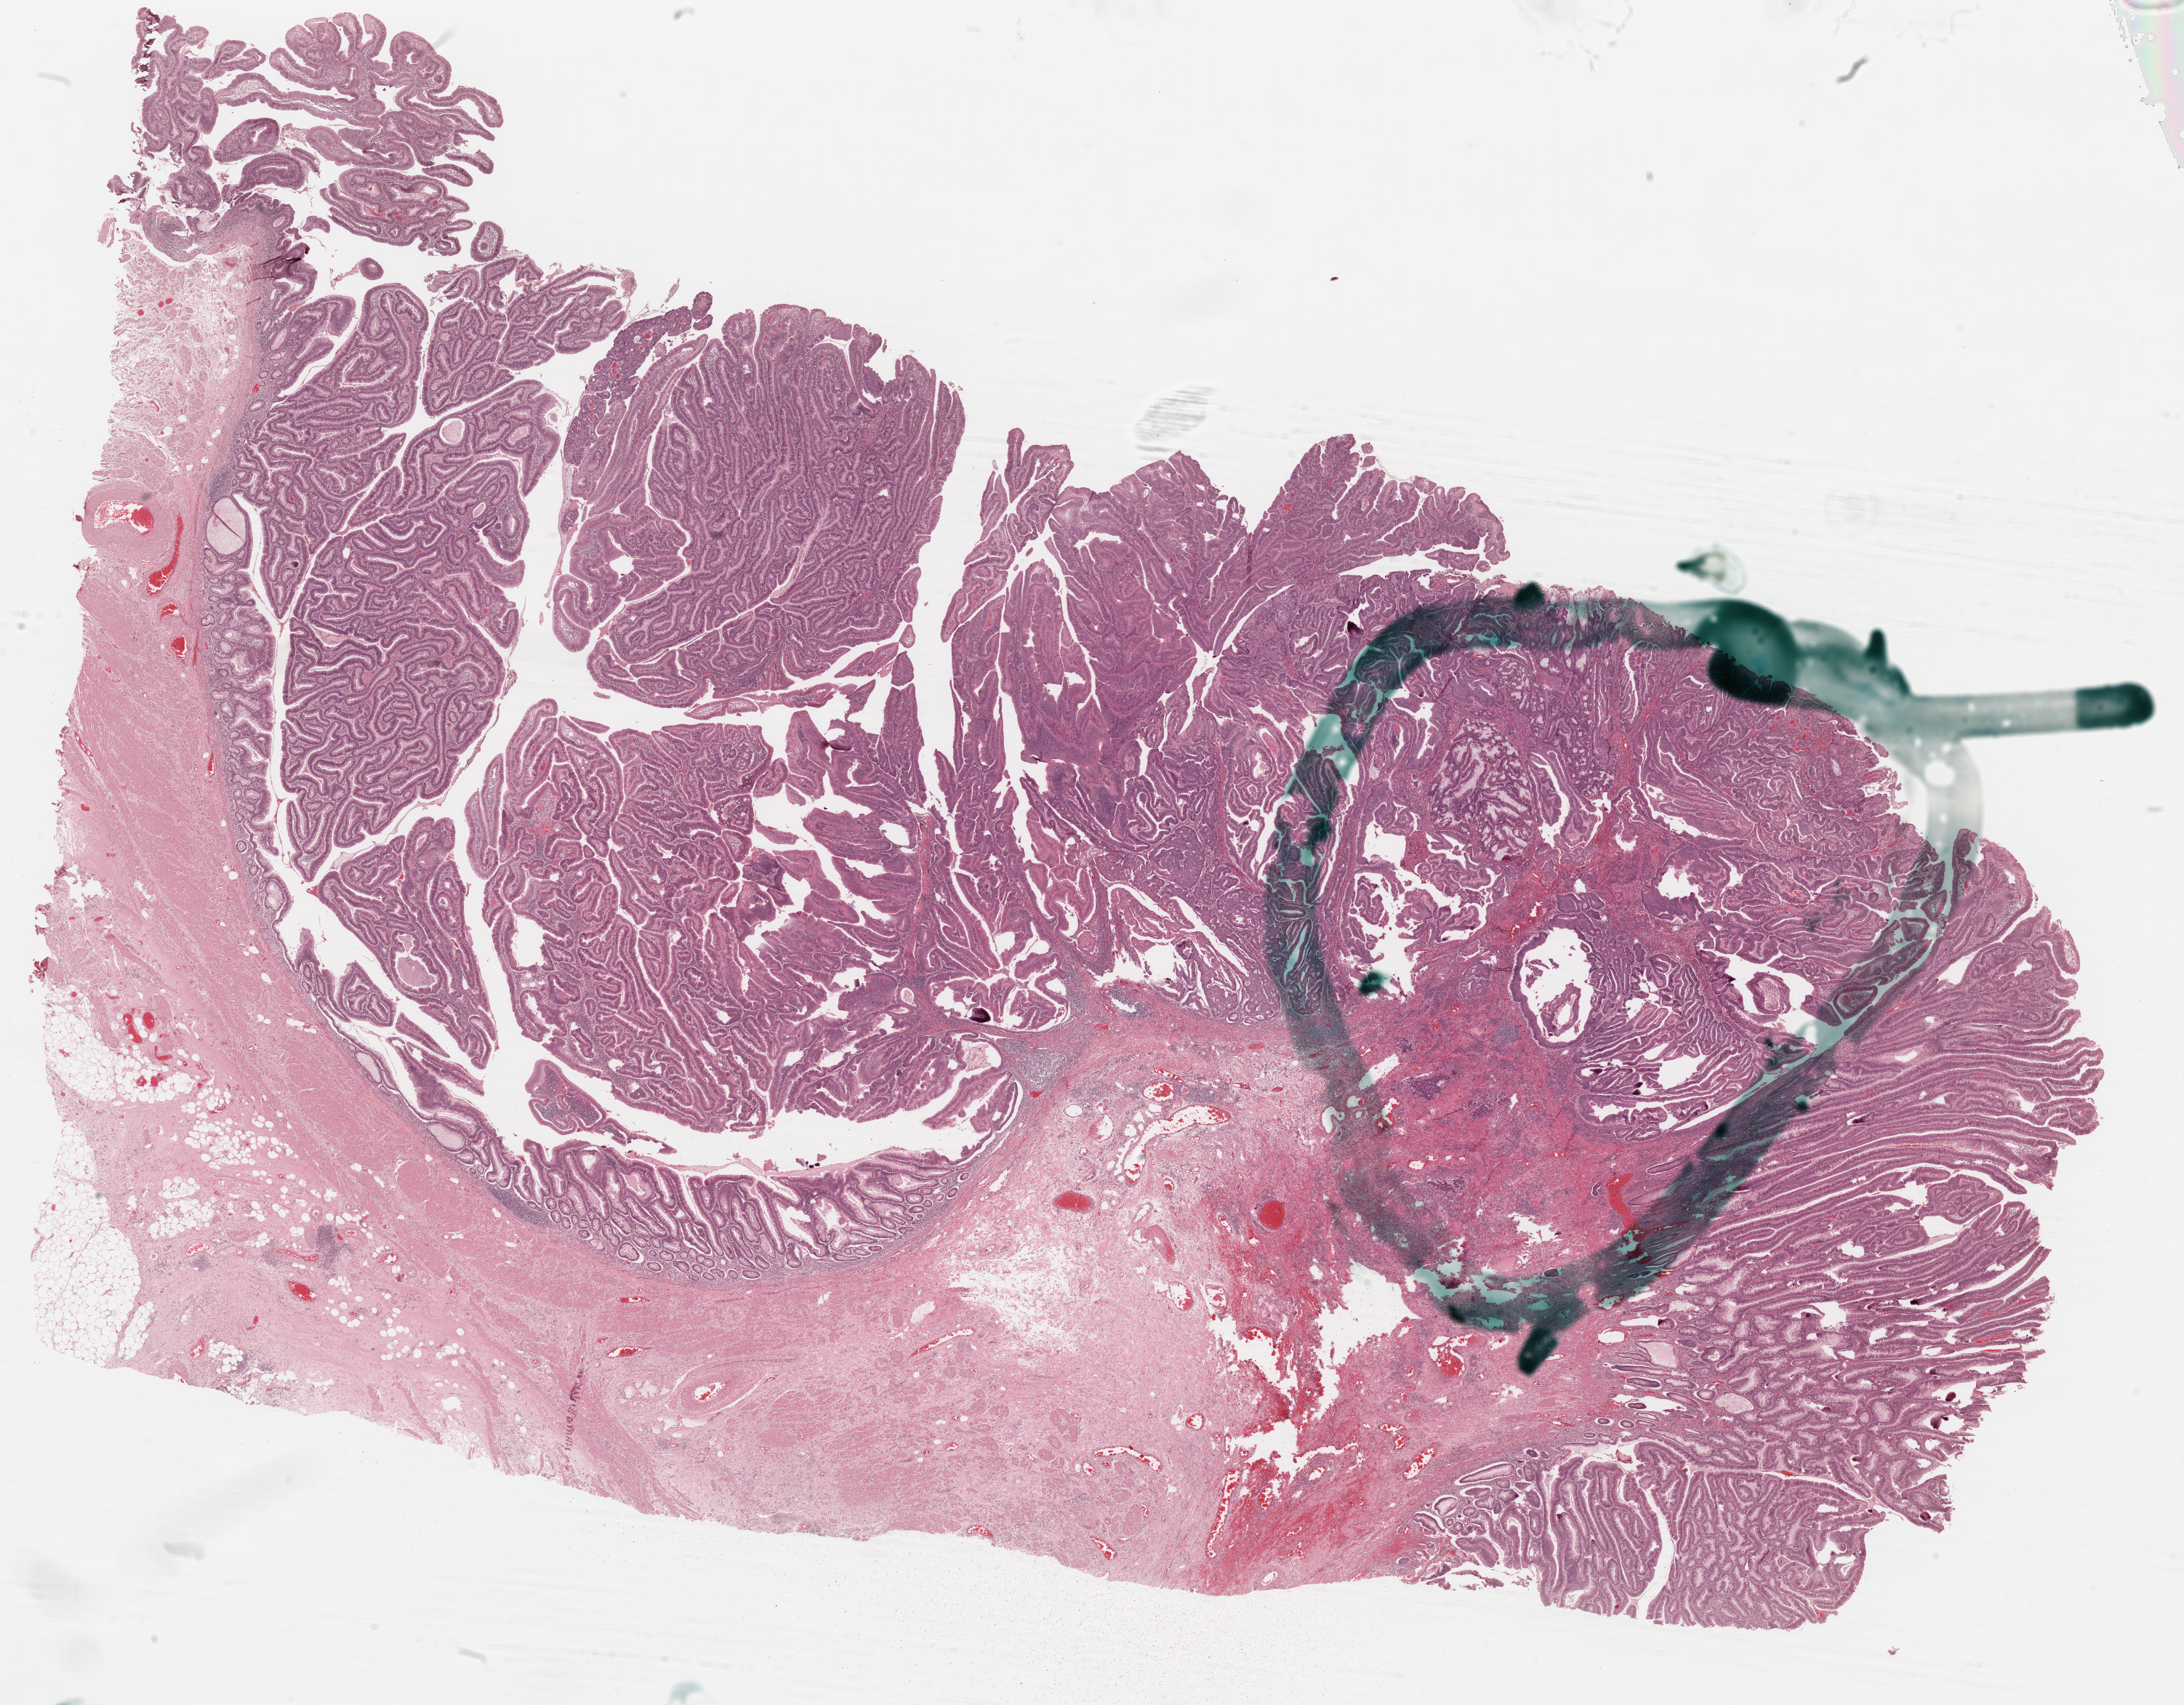
Digitized Hematoxylin and eosin (H&E) stained tissue section (whole slide), shown as a low-resolution overview of the whole scanned area (about 23.7 x 18.5 mm, from a 40x scan). Formalin-fixed paraffin-embedded (FFPE) diagnostic section. Colon, primary tumour sample. Female, age 71 years at initial diagnosis.
Diagnosis: Adenocarcinoma, NOS.